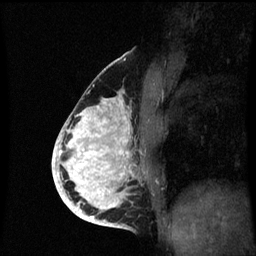
Breast MRI (dynamic contrast-enhanced), one sagittal slice. Position 33 of 60 along the scan axis. Dynamic contrast-enhanced series, image 2 of 3 at this slice position (ordered by acquisition). 1.5 T. TE 4.2 ms, TR 8.9 ms. 2 mm slice thickness. 256 × 256 image matrix, field of view 200 × 200 mm. Female patient, age 35 years. Case-level facts recorded for this patient, not image findings: setting: breast cancer imaged before/during neoadjuvant chemotherapy; receptor status: HR-positive, HER2-negative.
Structures marked on this image (semi-automatic segmentation, software-assisted and operator-edited):
- analysis volume of interest (the breast-tissue region the enhancement analysis was run in; not a lesion): box from (x=66, y=94) to (x=149, y=215) px
- tumour enhancement mask (voxels above the 70 % enhancement threshold inside the analysis volume of interest): (x=66, y=98)–(x=130, y=215)